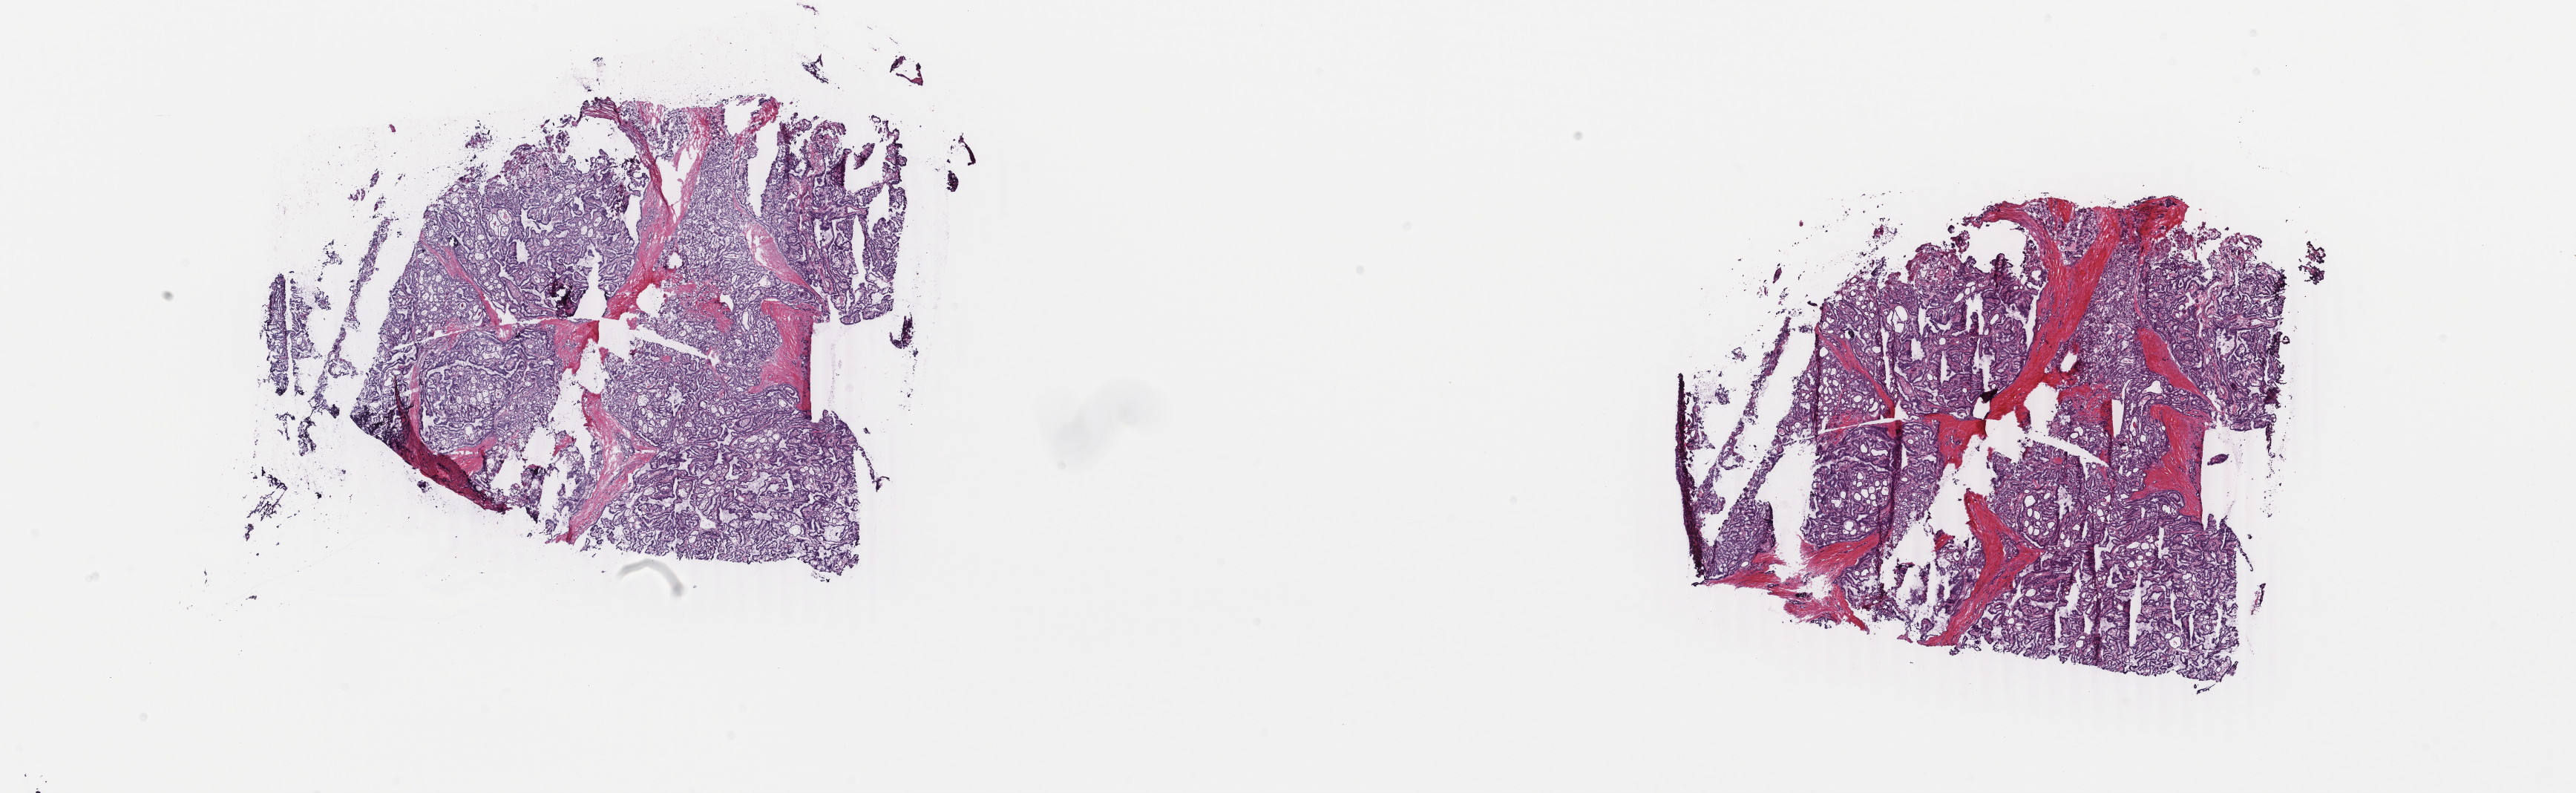
Whole-slide histology image, H&E-stained — shown as a low-resolution overview of the whole scanned area (about 27.6 x 8.5 mm); frozen section from the top of the tissue portion; primary tumour sample from the thyroid. Female, age 21 years at initial diagnosis. Composition of this section per pathologist review: tumour cells 85%, tumour nuclei 95%, normal cells 0%, stromal cells 15%, necrosis 0%. Infiltration values recorded for this section: lymphocyte infiltration 0%, monocyte infiltration 0%, neutrophil infiltration 0%.
- pathologic diagnosis: Papillary adenocarcinoma, NOS
- TNM: T3 N1a M0
- lymph nodes positive (case pathology): 8 of 20 examined
- AJCC pathologic stage: I